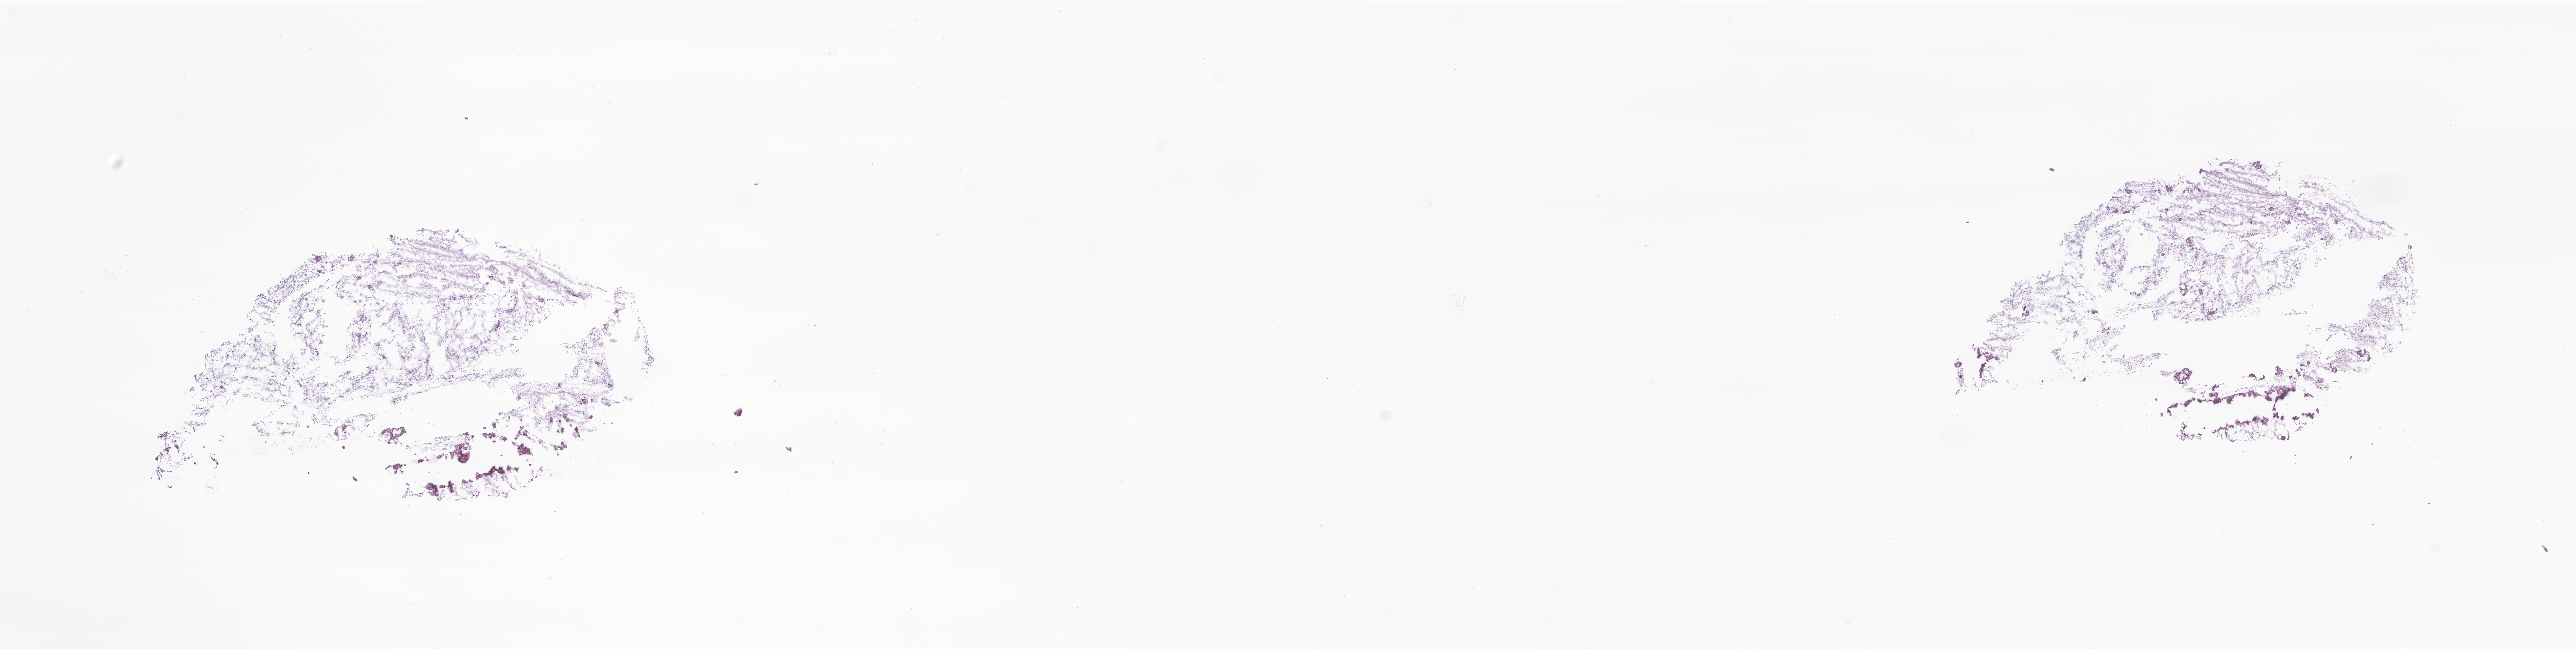
Digitized haematoxylin and eosin-stained section of tumor tissue from the brain — low-resolution overview of the scanned area, about 32.2 x 8.1 mm. Cryosection (OCT / tissue freezing medium). Patient: male, age 82 months (6 years 10 months).
Diagnosis (ICD-O-3 morphology term): Neoplasm, uncertain whether benign or malignant.